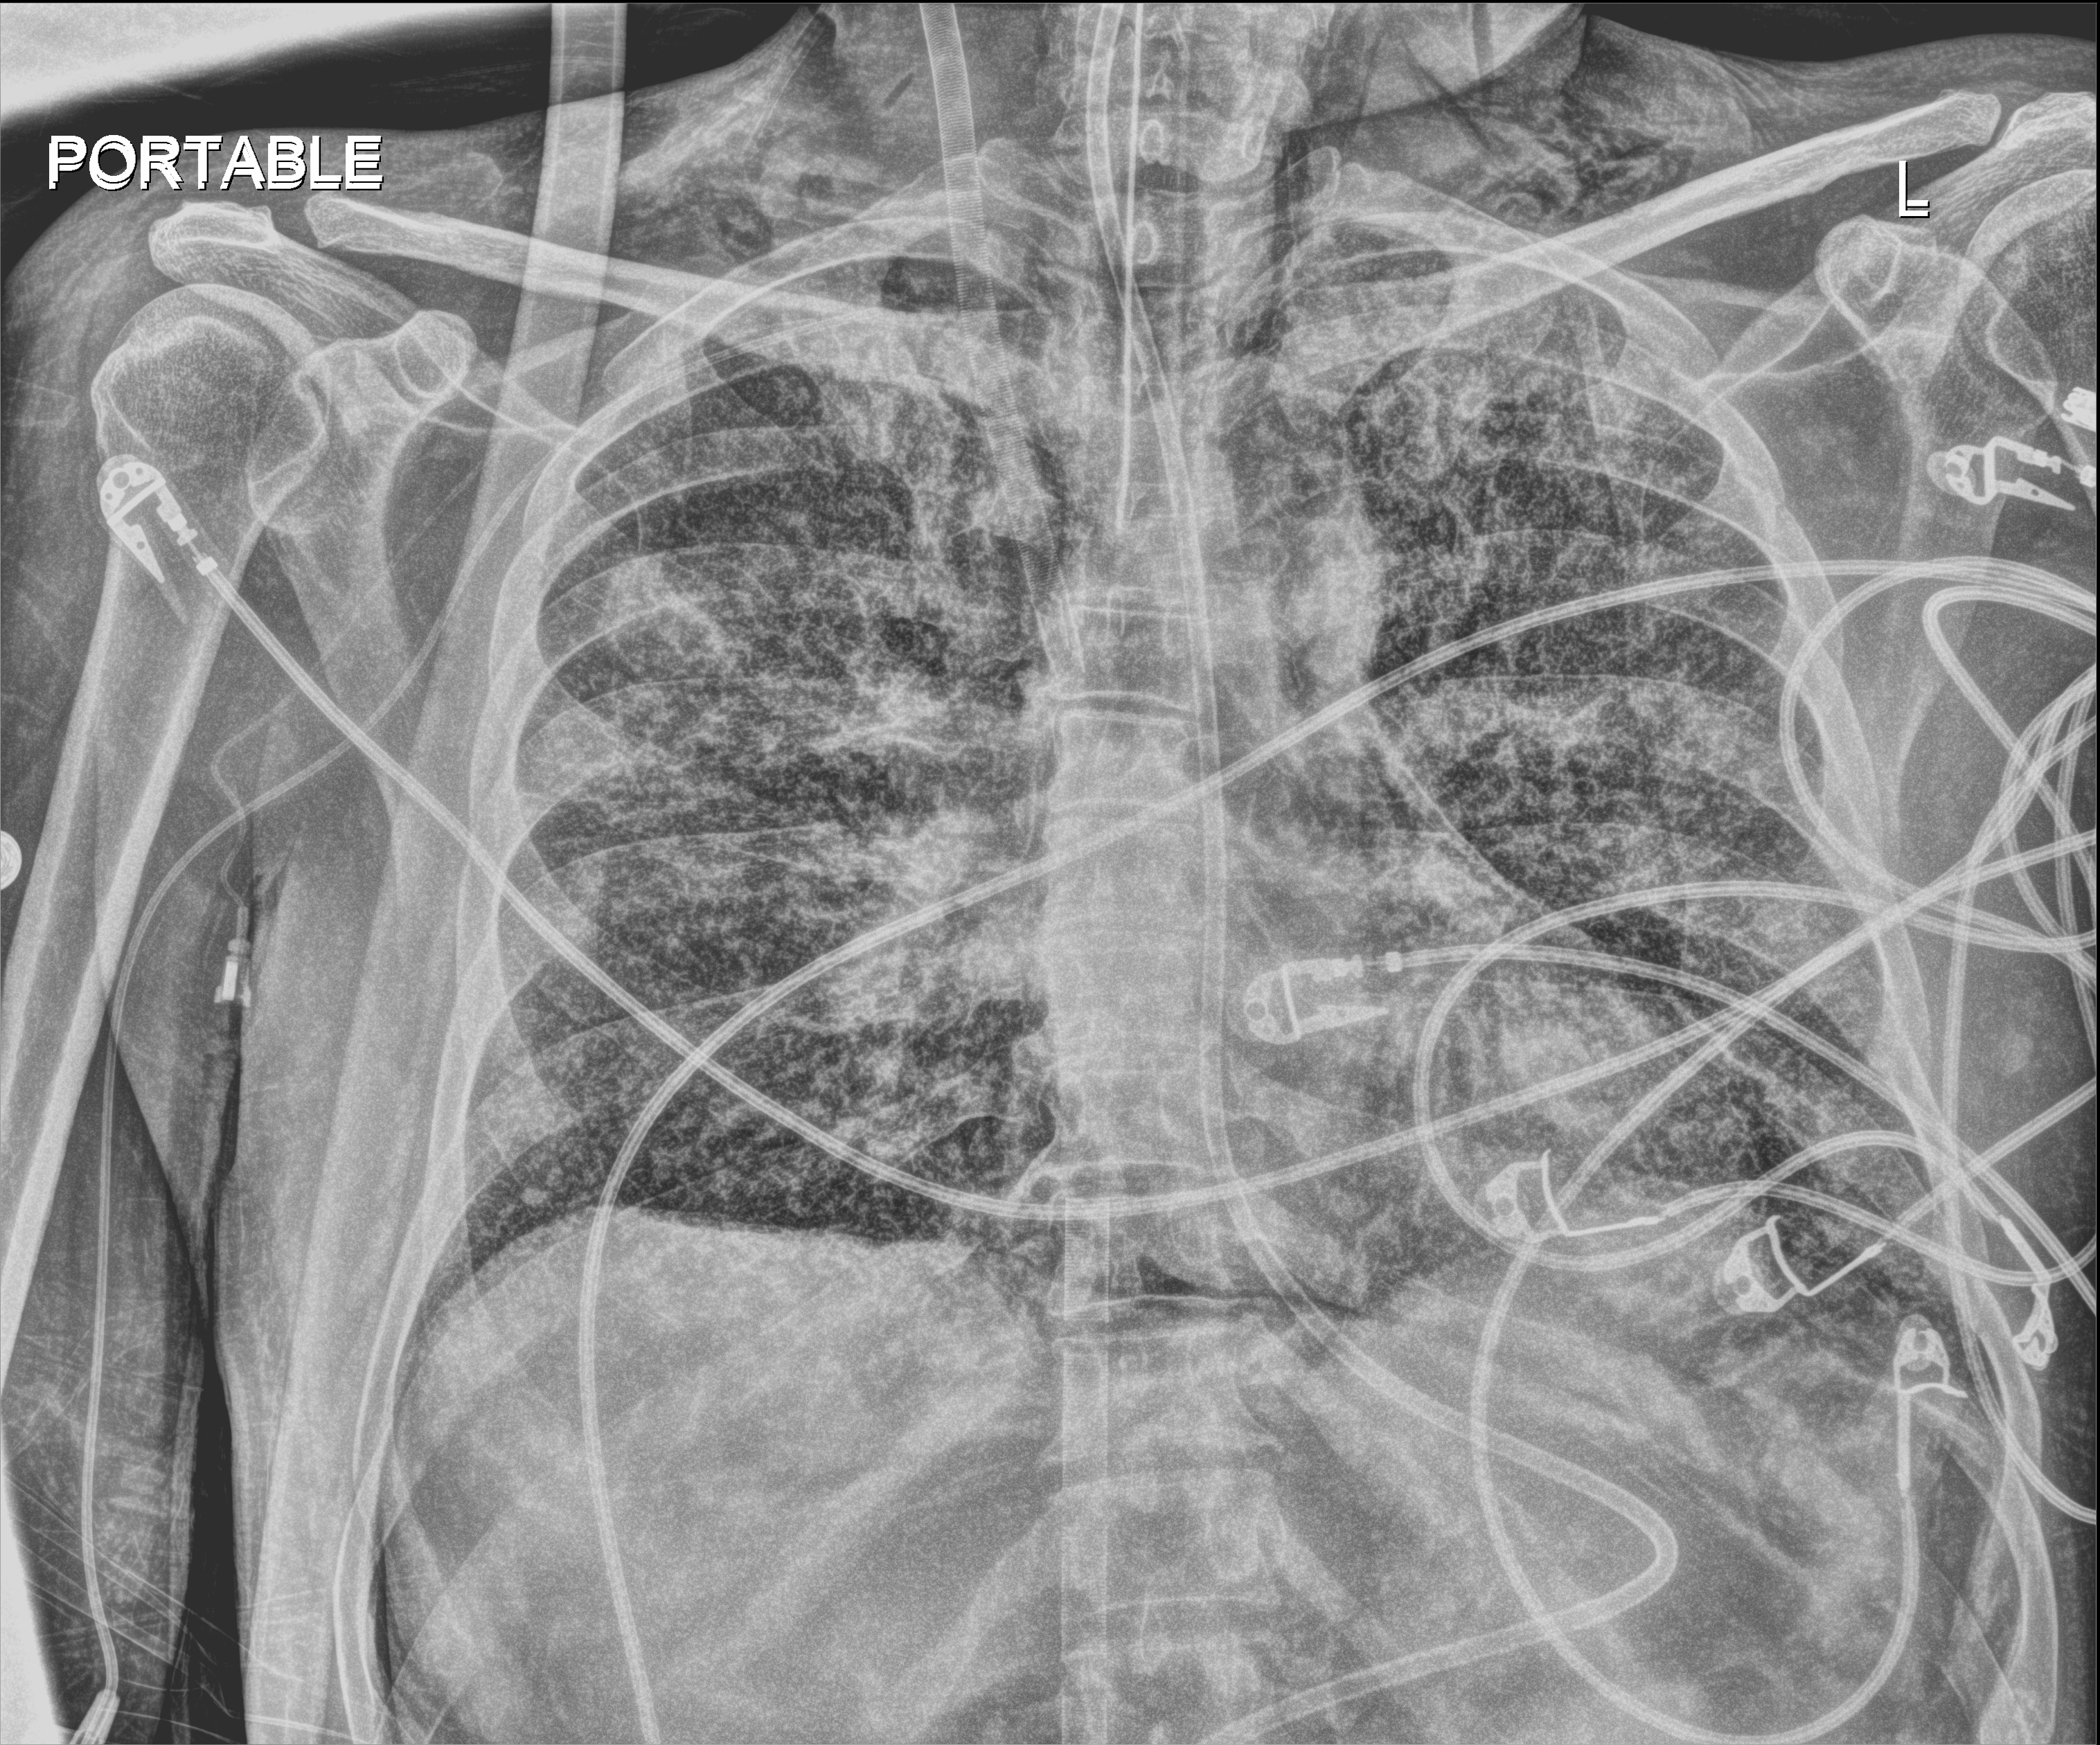
Bedside chest radiograph (digital radiography), anteroposterior (AP) projection. Patient hospitalised with COVID-19; male, aged 18–59 years.
Hospital-stay facts (about this admission, not read from this image; timing relative to this image not recorded):
- length of hospital stay: 42 days
- chronic kidney disease (admission record): no